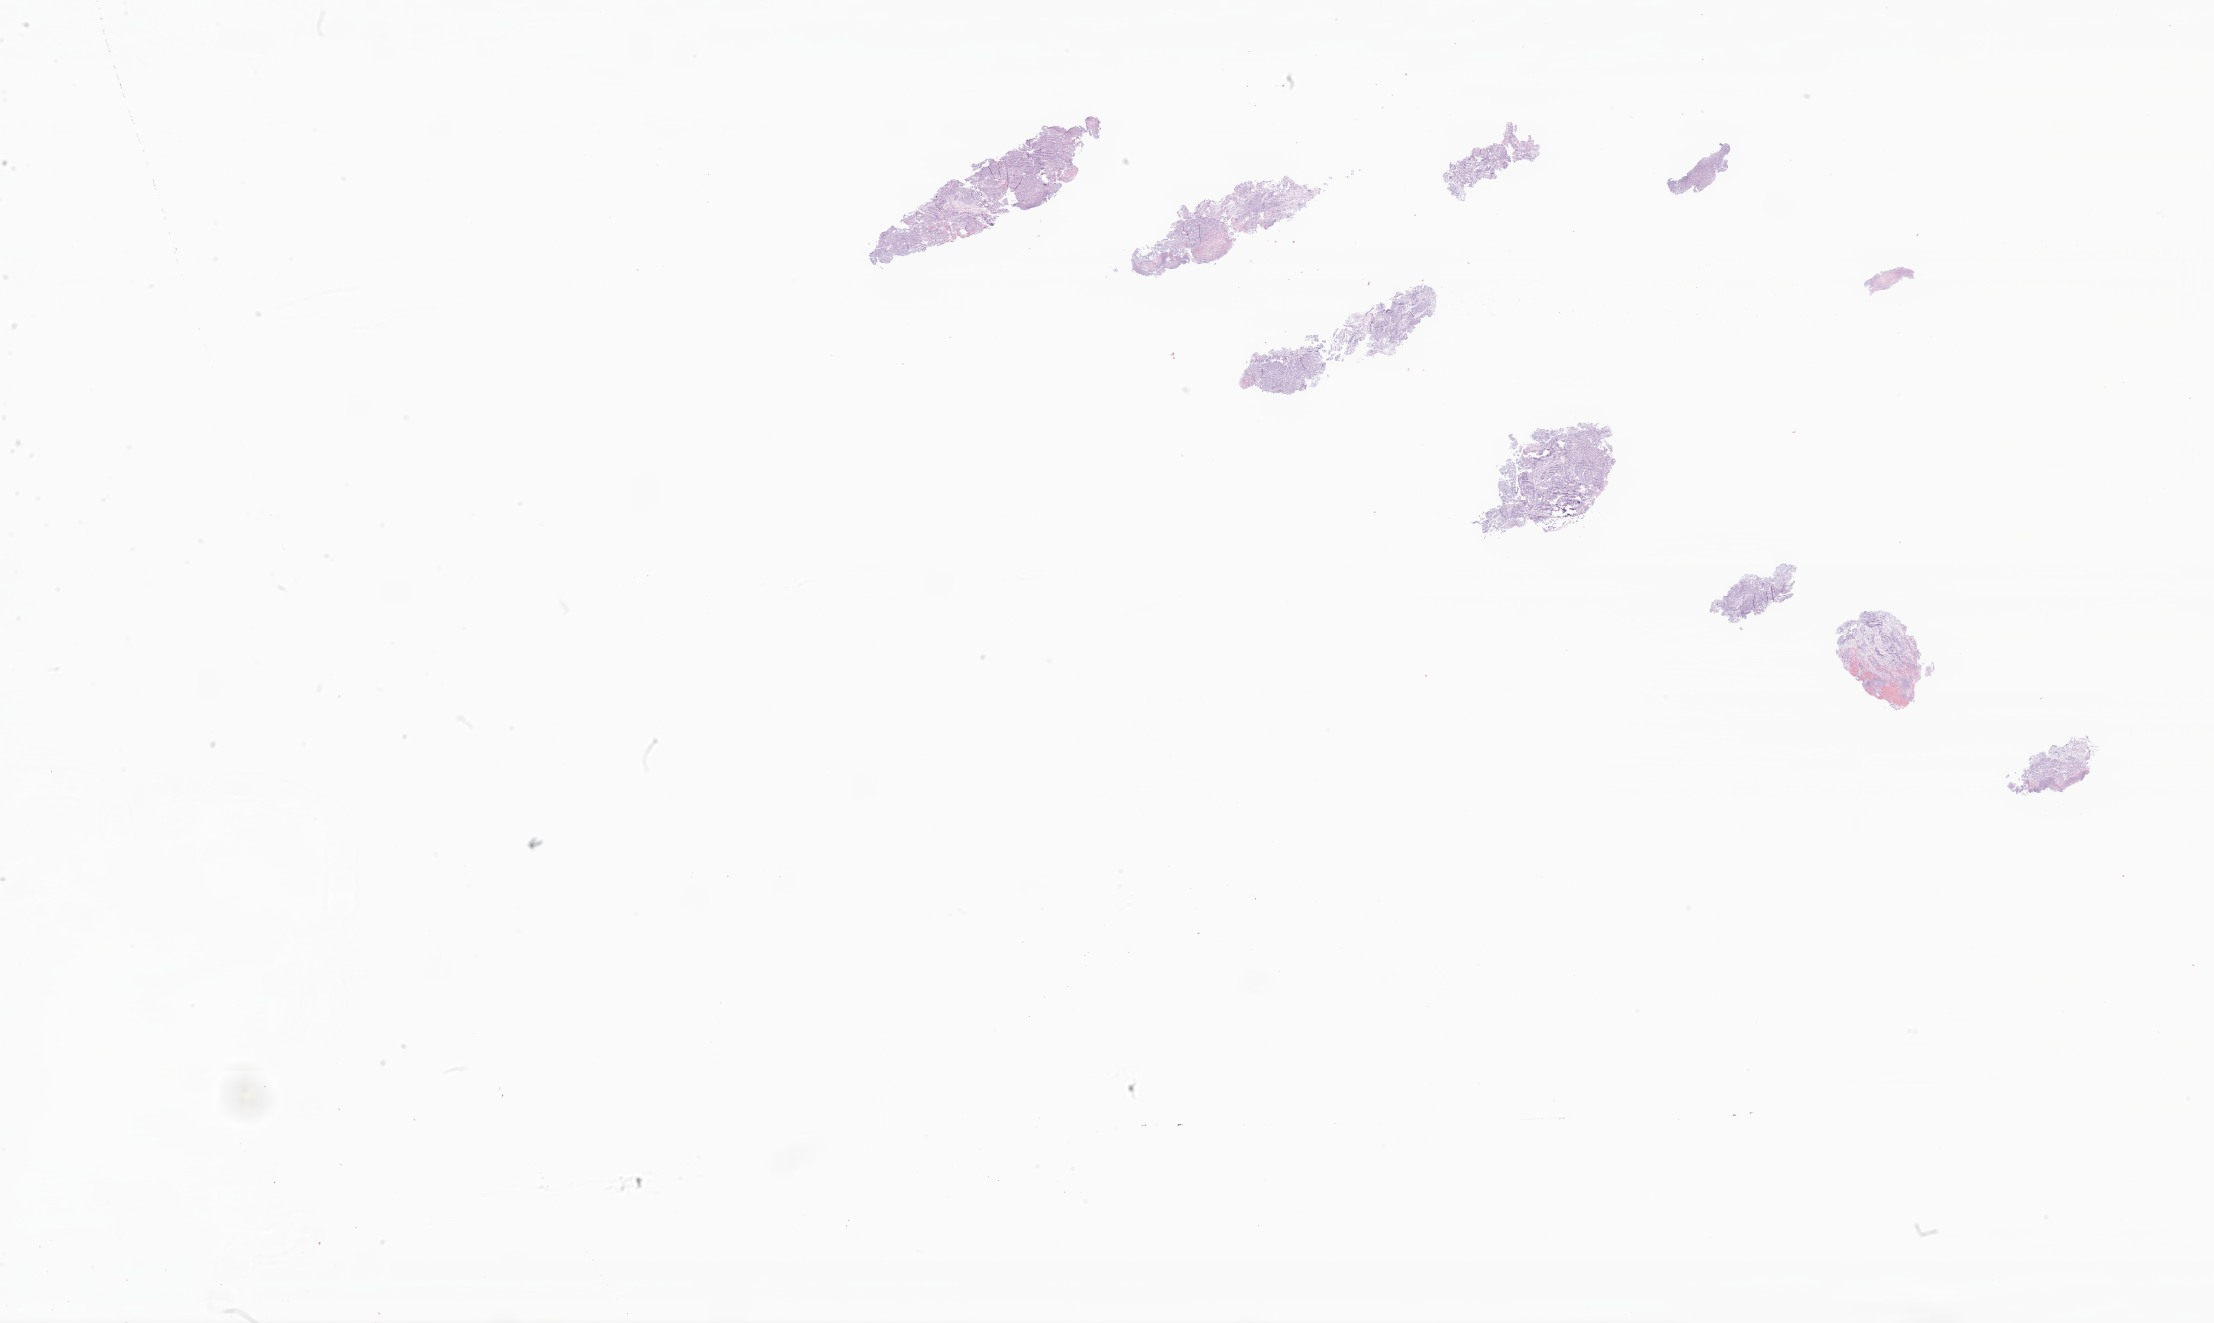
Whole-slide image, H&E stain of tumor tissue from the colon, a low-resolution overview of the entire scanned area, about 37.3 x 22.3 mm; formalin-fixed, paraffin-embedded (FFPE) tissue. Female patient, age 196 months (16 years 4 months).
* diagnosis (ICD-O-3 morphology term): Neoplasm, malignant